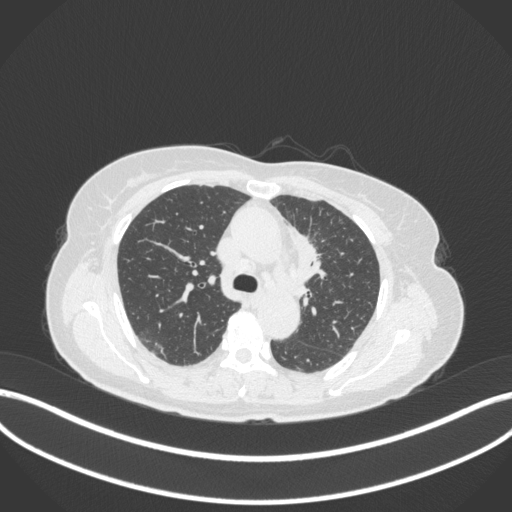
Chest CT, one axial slice; lung window (W 1500 / L -600 HU); 512 × 512 image matrix, field of view 400 × 400 mm. Patient: female, 65 years. From the clinical record (not read from this slice): clinical TNM (as recorded): T2a N0 M0.
Structures marked on this image (rectangle marked by the reading radiologist):
- lung tumour (recorded histology: adenocarcinoma): box from (x=296, y=233) to (x=324, y=284) px